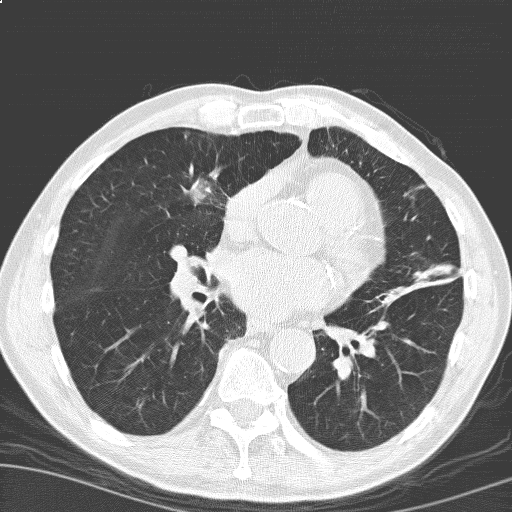
Low-dose screening chest CT, one axial slice; position 89 of 184 along the scan axis; 120 kVp; lung window (W 1500 / L -600 HU); 3.2 mm slice thickness; 512 × 512 image matrix, field of view 329 × 329 mm.
Annotated regions visible in this slice (manually delineated by an expert):
- lesion 1 (tumor, upper lobe of right lung): bounding box [x1, y1, x2, y2] px = [188, 174, 215, 203]